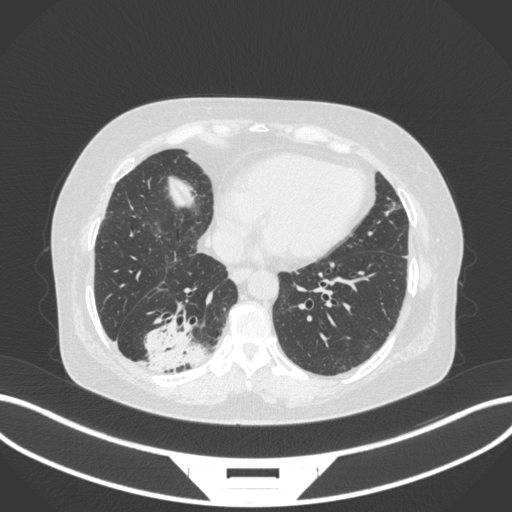
Chest CT, one axial slice. Position 71 of 303 along the scan axis. Lung window (W 1500 / L -600 HU). 1 mm slice thickness. 512 × 512 image matrix. Female patient, age 65 years. Case-level facts recorded for this patient, not image findings: clinical TNM (as recorded): T2b N1 M0; histopathological grade: G1.
Annotated regions visible in this slice (rectangle marked by the reading radiologist):
- lung tumour (recorded histology: adenocarcinoma): bounding box [x1, y1, x2, y2] px = [140, 319, 212, 375]